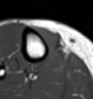
MRI of an extremity soft-tissue mass, one axial slice; position 22 of 54 along the scan axis; MR volume resampled by the dataset authors to the PET/CT grid (not the native acquisition matrix); 3.27 mm slice thickness; 93 × 99 image matrix, field of view 91 × 97 mm. Female patient. Case-level facts recorded for this patient, not image findings: histological type: undifferentiated – high grade; grade: high; site of the primary tumour: right thigh.
Annotated regions visible in this slice (expert contour drawn on MRI and transferred to this co-registered scan by the dataset authors):
- gross tumour volume (mass): bounding box [x1, y1, x2, y2] px = [32, 25, 64, 60]